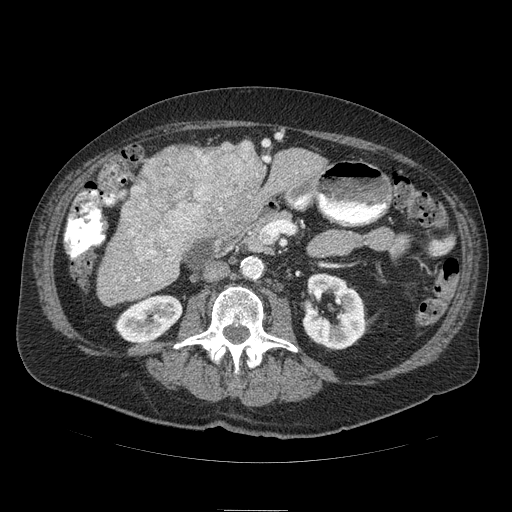
Contrast-enhanced abdominal CT (liver protocol), one axial slice; 120 kVp; soft-tissue window (W 400 / L 40 HU); 2.5 mm slice thickness; 512 × 512 image matrix, field of view 440 × 440 mm. From the clinical record (not read from this slice): diagnosis: hepatocellular carcinoma (patient treated with transarterial chemoembolisation; whether this scan precedes or follows treatment is not stated here); TNM stage (as recorded): Stage-IIIA; Child-Pugh class: B; tumour nodularity: multinodular.
Outlined on this slice (semi-automatic segmentation, software-assisted and operator-edited):
- liver parenchyma outside the tumour (the mass and vessels are separate outlines, so this box may not span the whole liver): bounding box [x1, y1, x2, y2] px = [98, 140, 326, 302]
- mass: [124, 142, 266, 273]
- liver vessels: [136, 141, 270, 281]